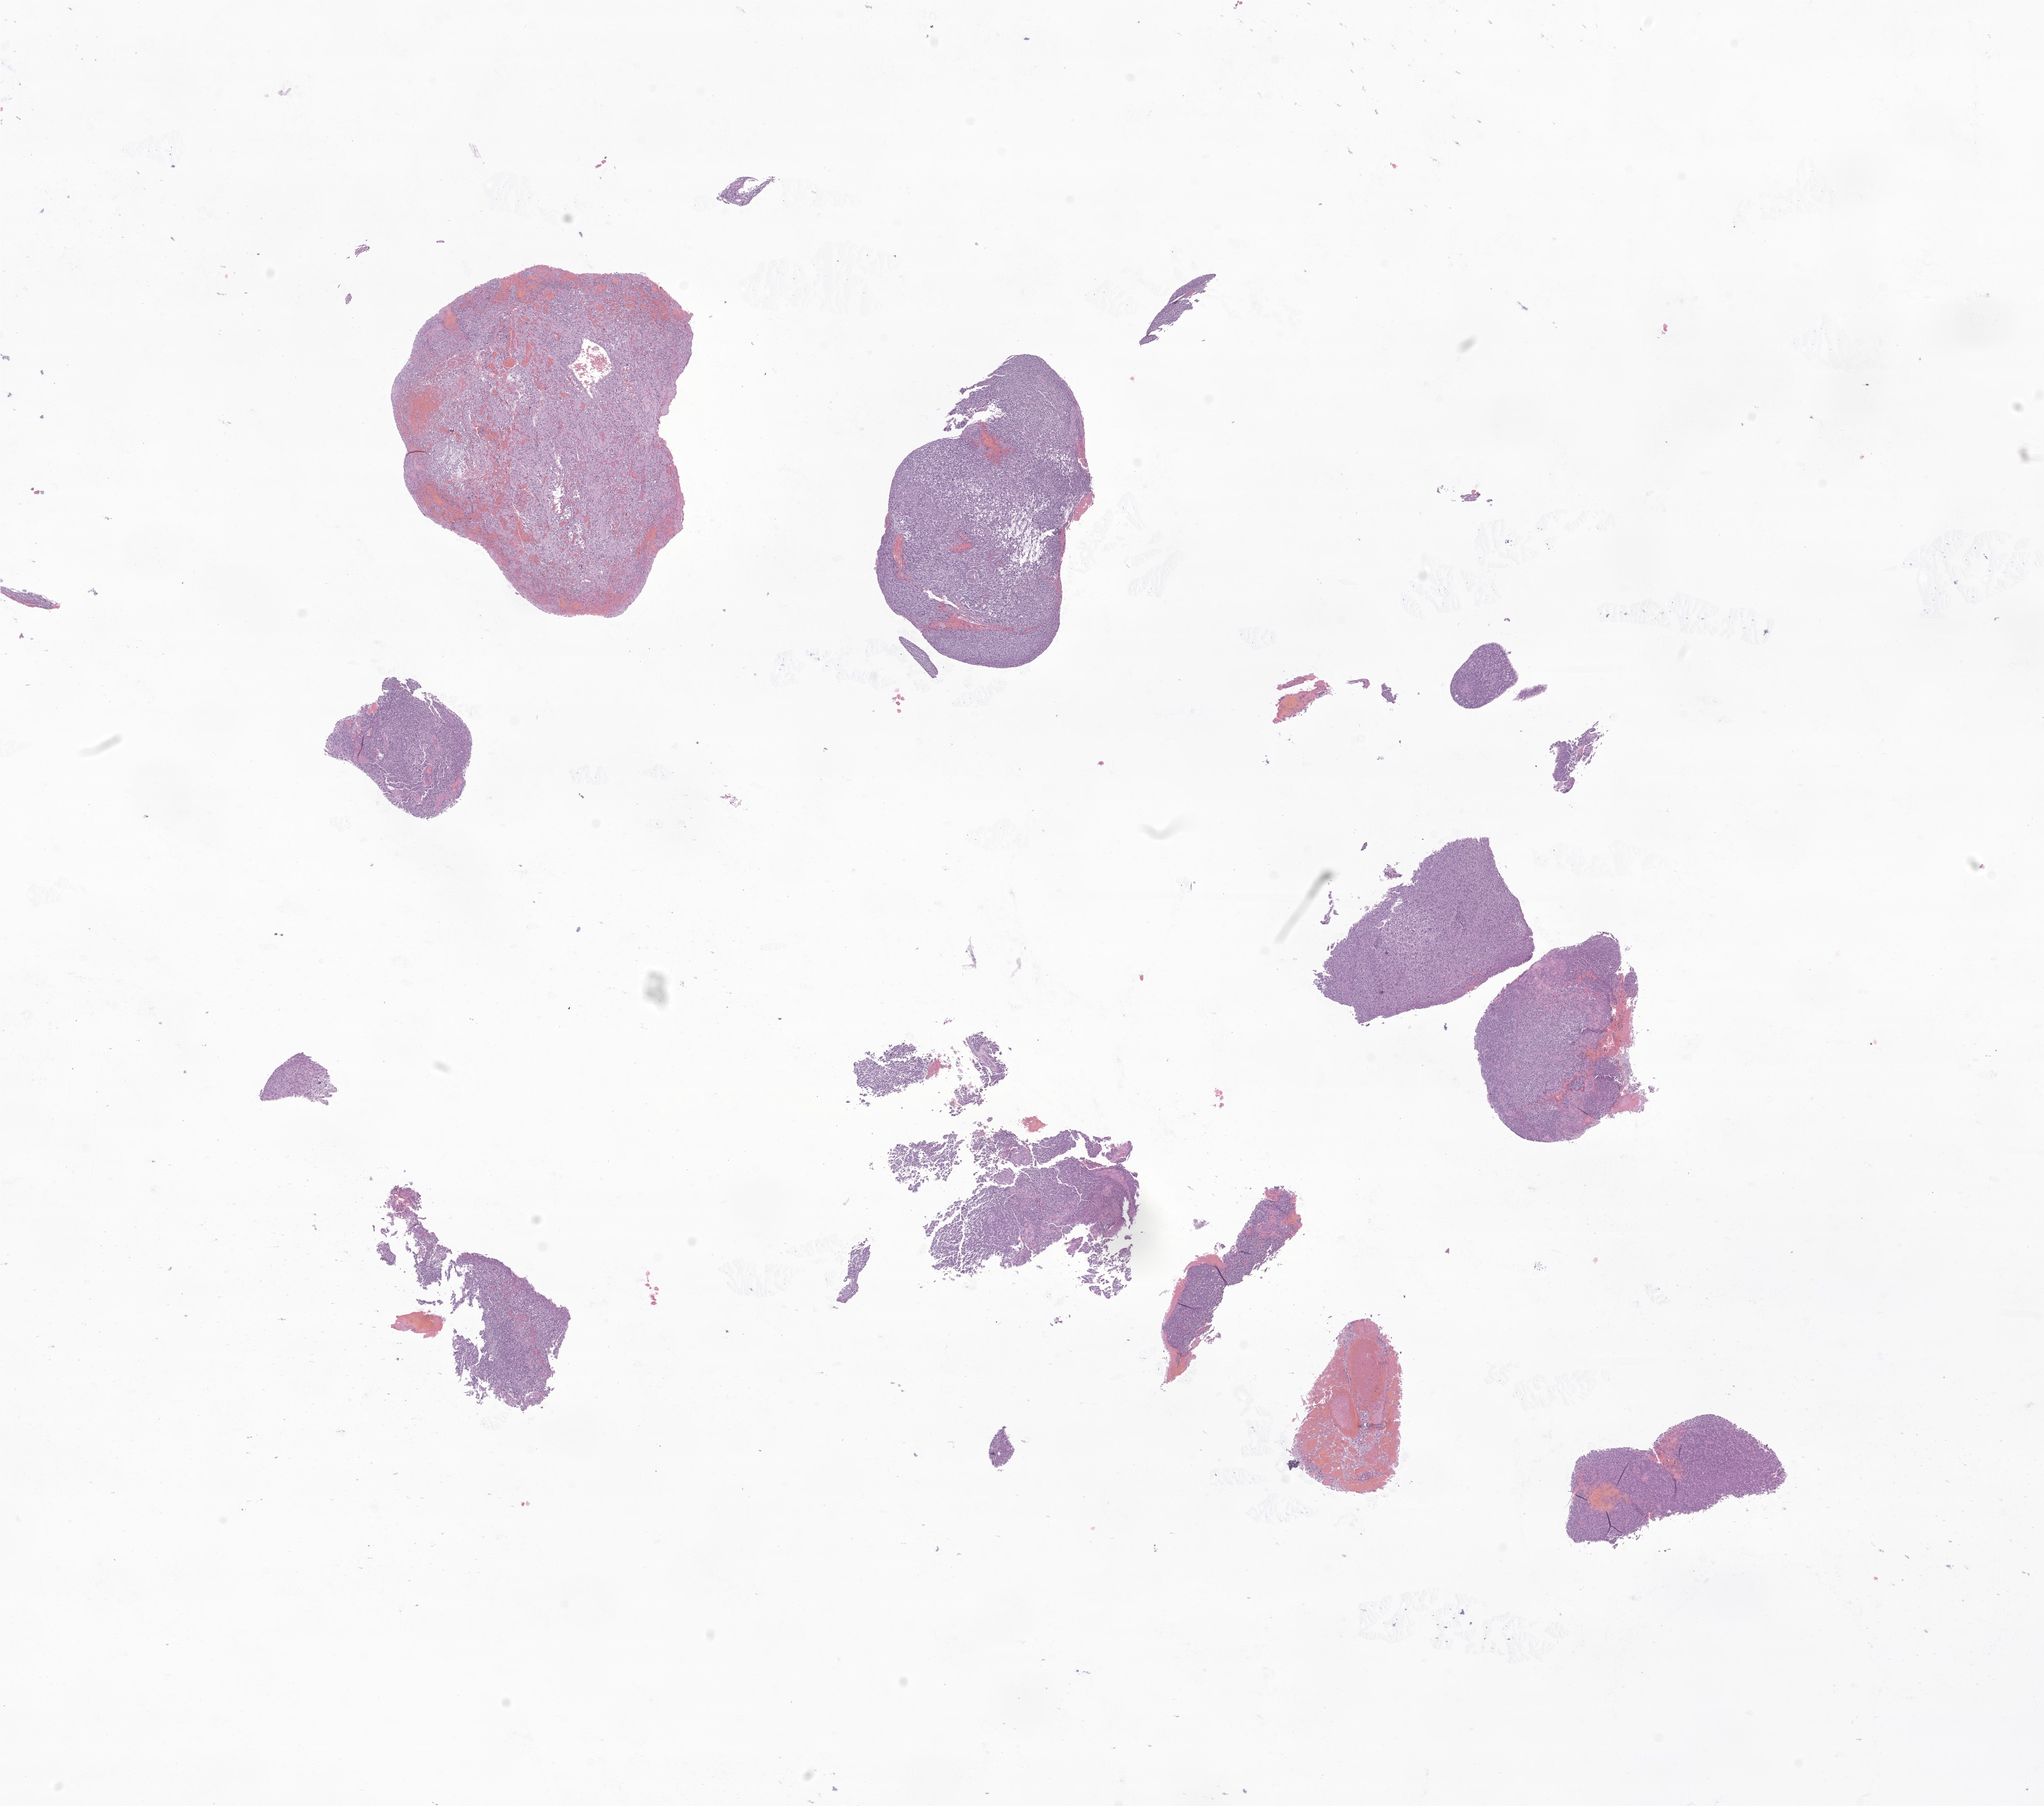
Whole-slide image, haematoxylin and eosin stain of tumor tissue from the frontal lobe — shown as a low-resolution overview of the whole scanned area (about 15.2 x 13.4 mm); formalin-fixed, paraffin-embedded (FFPE) tissue. Patient female; age 56 months (4 years 8 months).
- diagnosis: Glioma, malignant